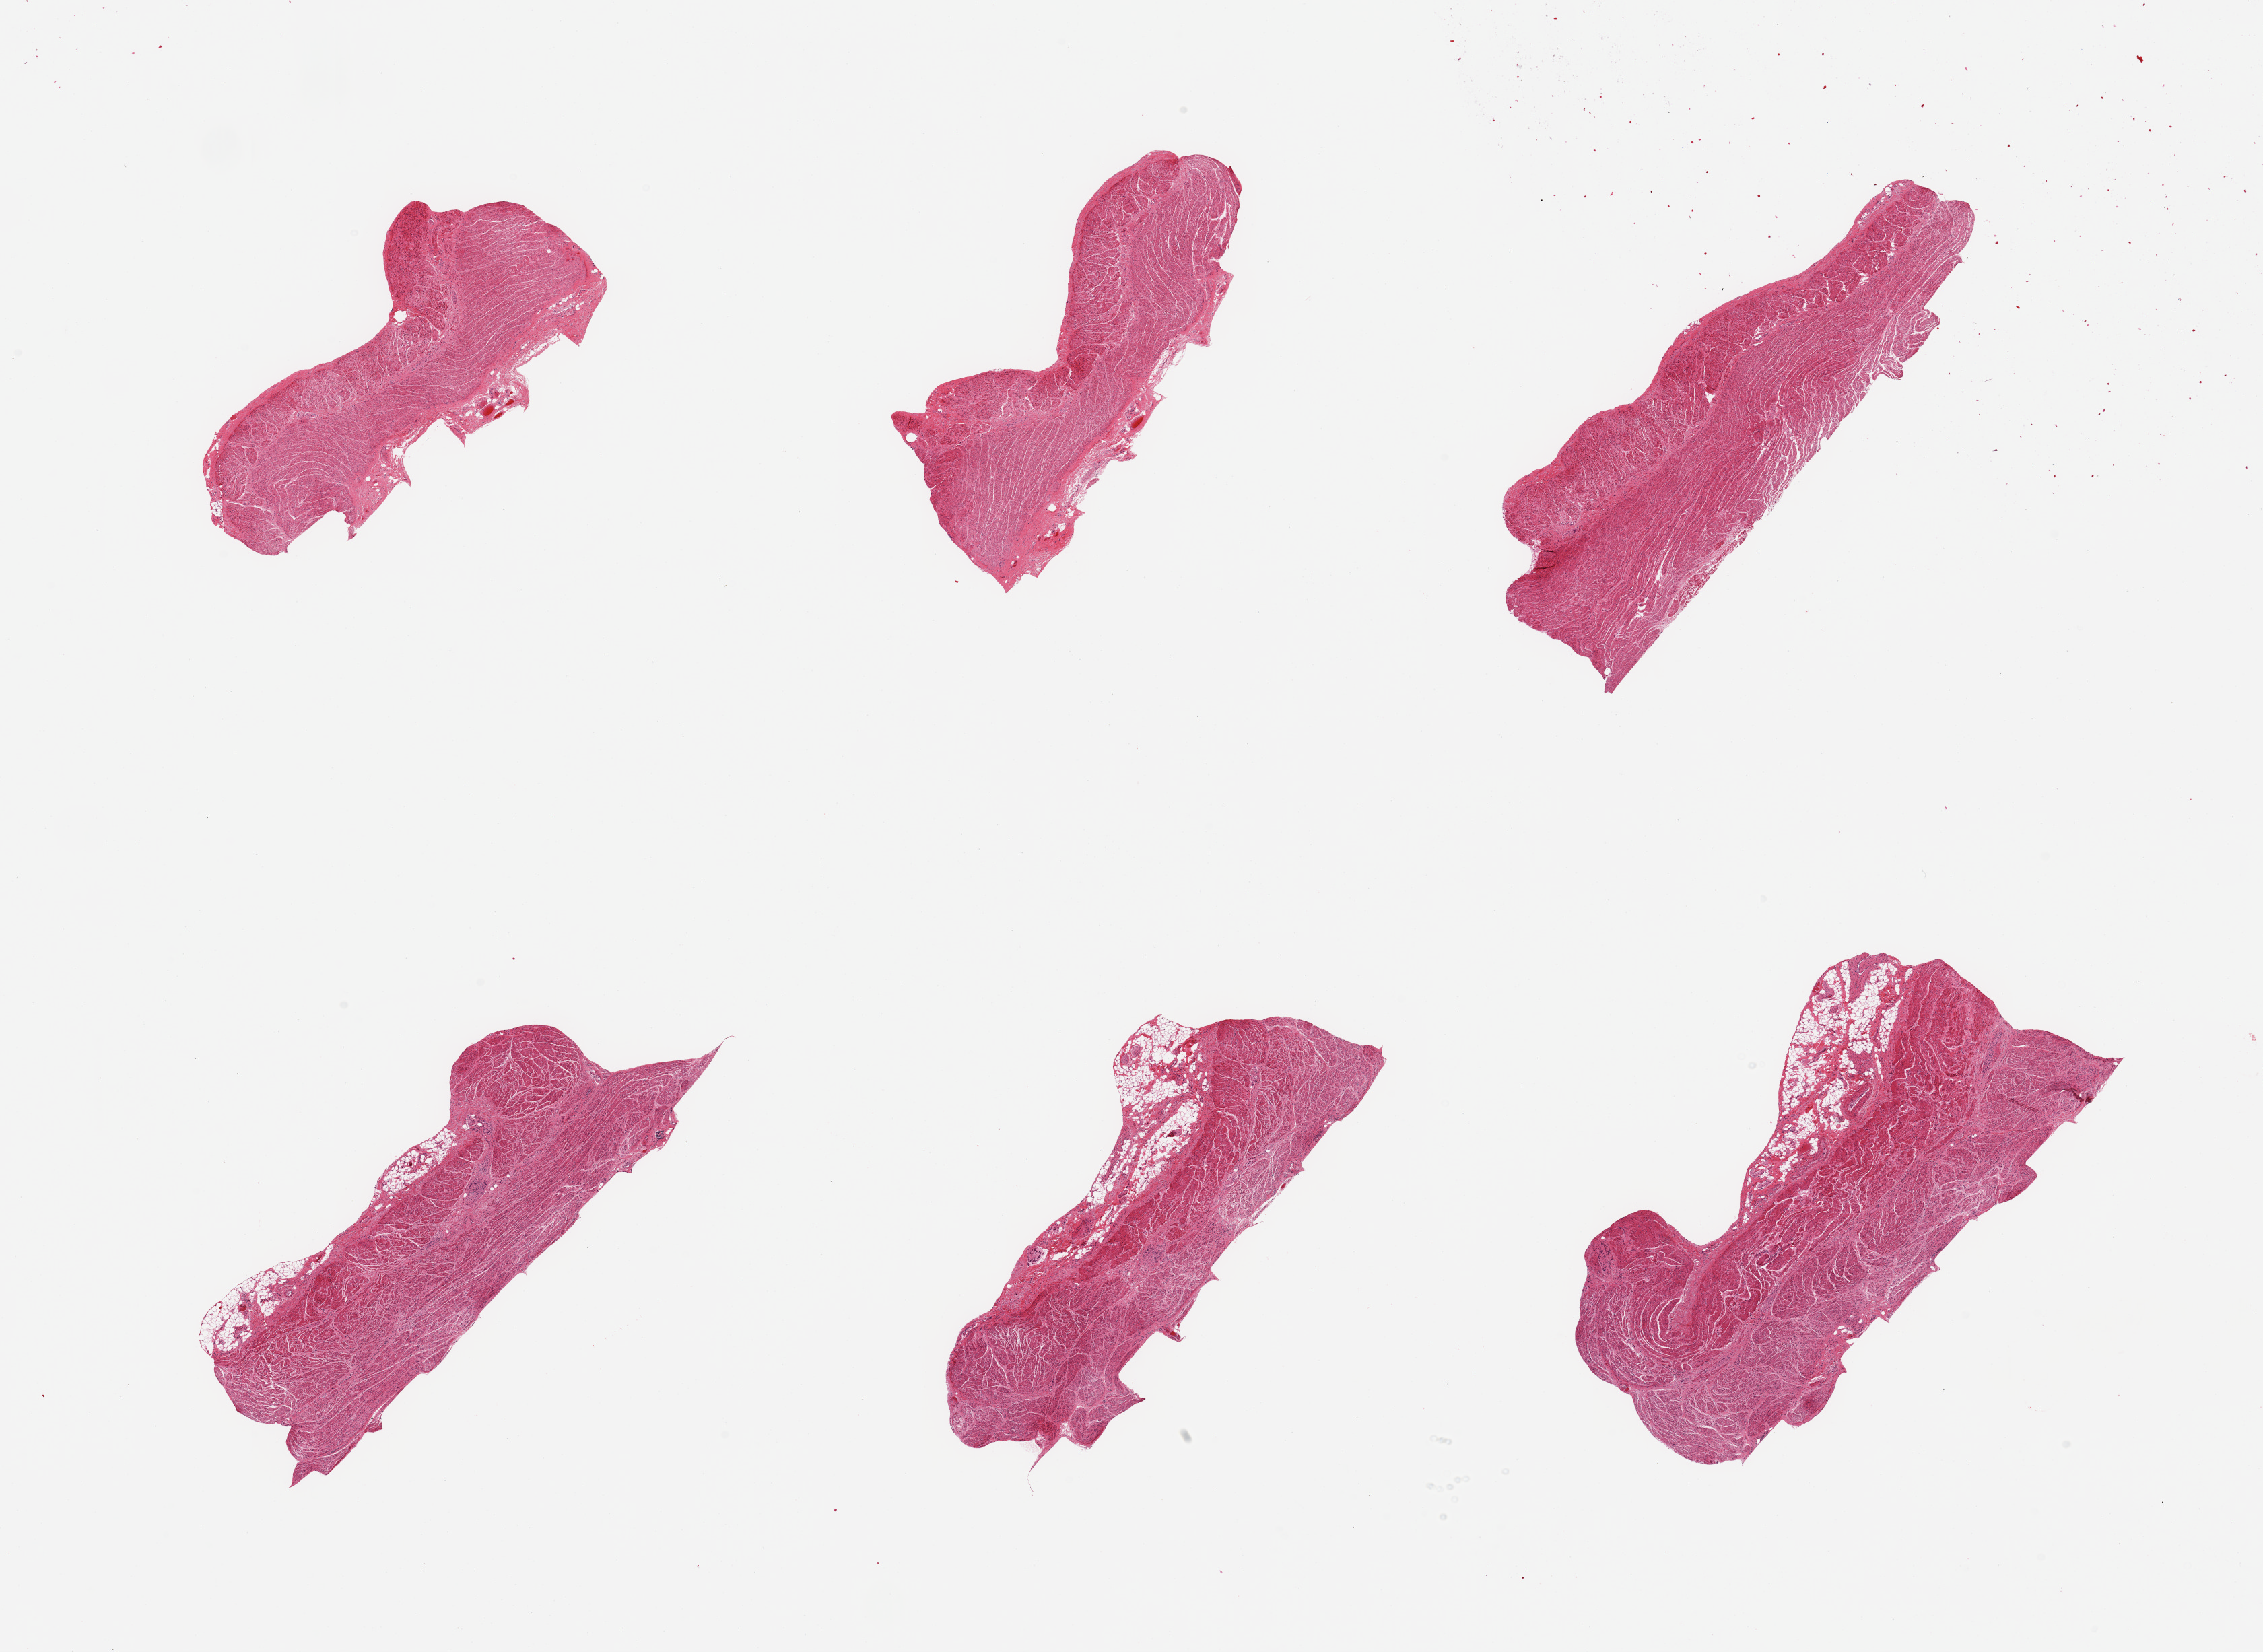
H&E whole-slide image, brightfield — whole scanned area (about 26.6 x 19.4 mm) shown as a low-resolution overview, PAXgene-fixed, paraffin-embedded tissue, section of gastroesophageal junction (target tissue), donor tissue sample. Donor: male.
Pathologist's review note for this sample: 6 pieces; up to 1 mm external fat on 2 pieces.